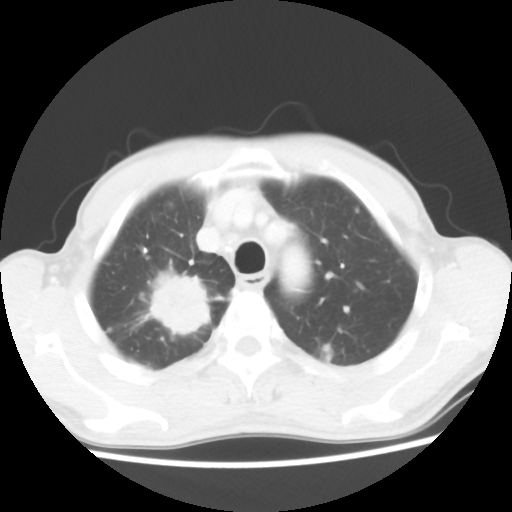
Chest CT, one axial slice. Reconstruction kernel STANDARD. Lung window (W 1500 / L -600 HU). 5 mm slice thickness. 512 × 512 image matrix. Patient: male, 66 years. From the clinical record (not read from this slice): clinical TNM (as recorded): T2 N0 M1a.
Annotated regions visible in this slice (rectangle marked by the reading radiologist):
- lung tumour (recorded histology: adenocarcinoma): bounding box <137,265,219,339> (left, top, right, bottom; pixels)